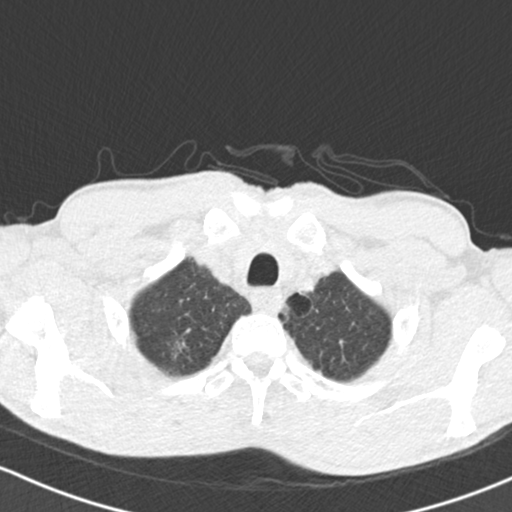
Chest CT (low-dose screening protocol), one axial image; baseline screening round; lung window (W 1500 / L -600 HU); slice 26 of 151 in the series. Male participant, aged 64 years at enrolment. Current smoker at enrolment.
Expert-annotated lung lesion, box from (x=147, y=325) to (x=201, y=381) px. Reader record for this screening exam (exam-level; its link to the box is not recorded): non-calcified nodule or mass ≥4 mm, right upper lobe, 13 × 11 mm, spiculated (stellate) margins, soft tissue attenuation. Official screen result: positive, change unspecified: nodule(s) >= 4 mm or enlarging nodule(s), mass(es), or other non-specific abnormalities suspicious for lung cancer. Participant outcome: lung cancer diagnosed 161 days after this screen — adenocarcinoma, NOS, right upper lobe, poorly differentiated (G3), stage IA (AJCC 6th edition), 13 mm at pathology.